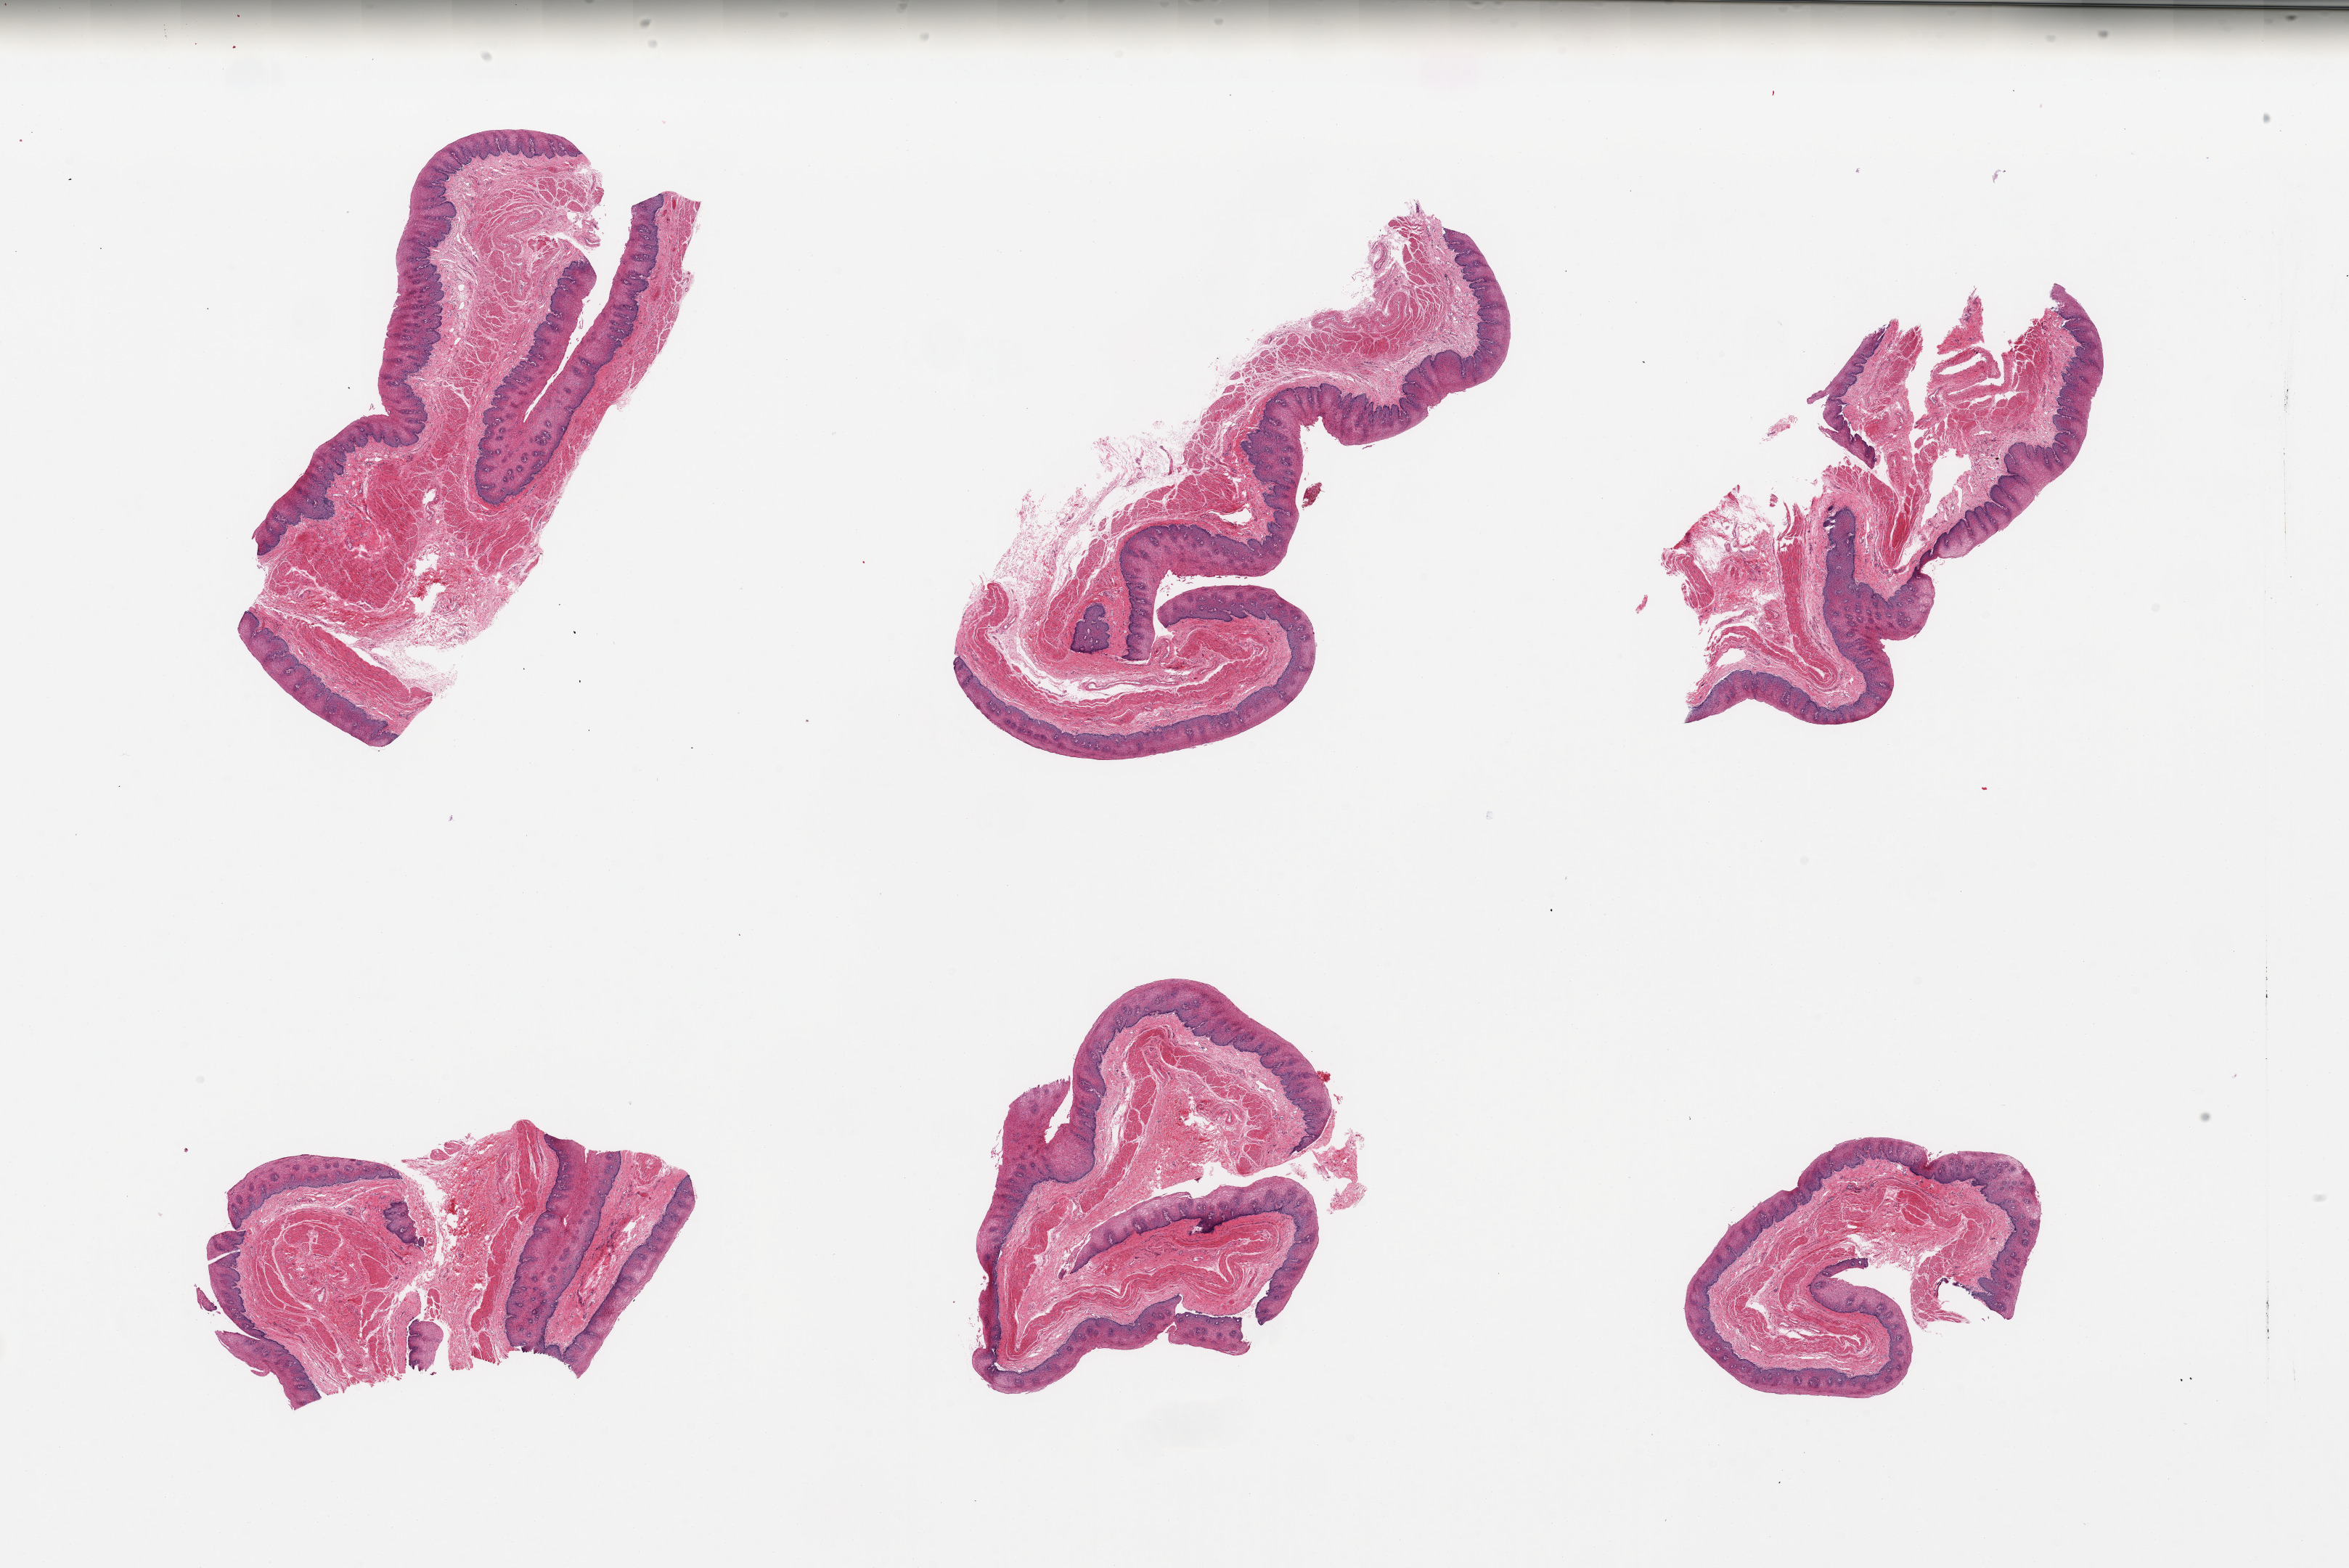
Hematoxylin and eosin (H&E) whole-slide image, whole scanned area (about 25.6 x 17.1 mm, acquisition: 20x scan) shown as a low-resolution overview, PAXgene-fixed, paraffin-embedded tissue, target tissue: esophageal mucous membrane, tissue donor sample. Donor: male.
Review note (as recorded): 6 pieces, squamous mucosa up to ~0.5mm, ~20-30% thickness.